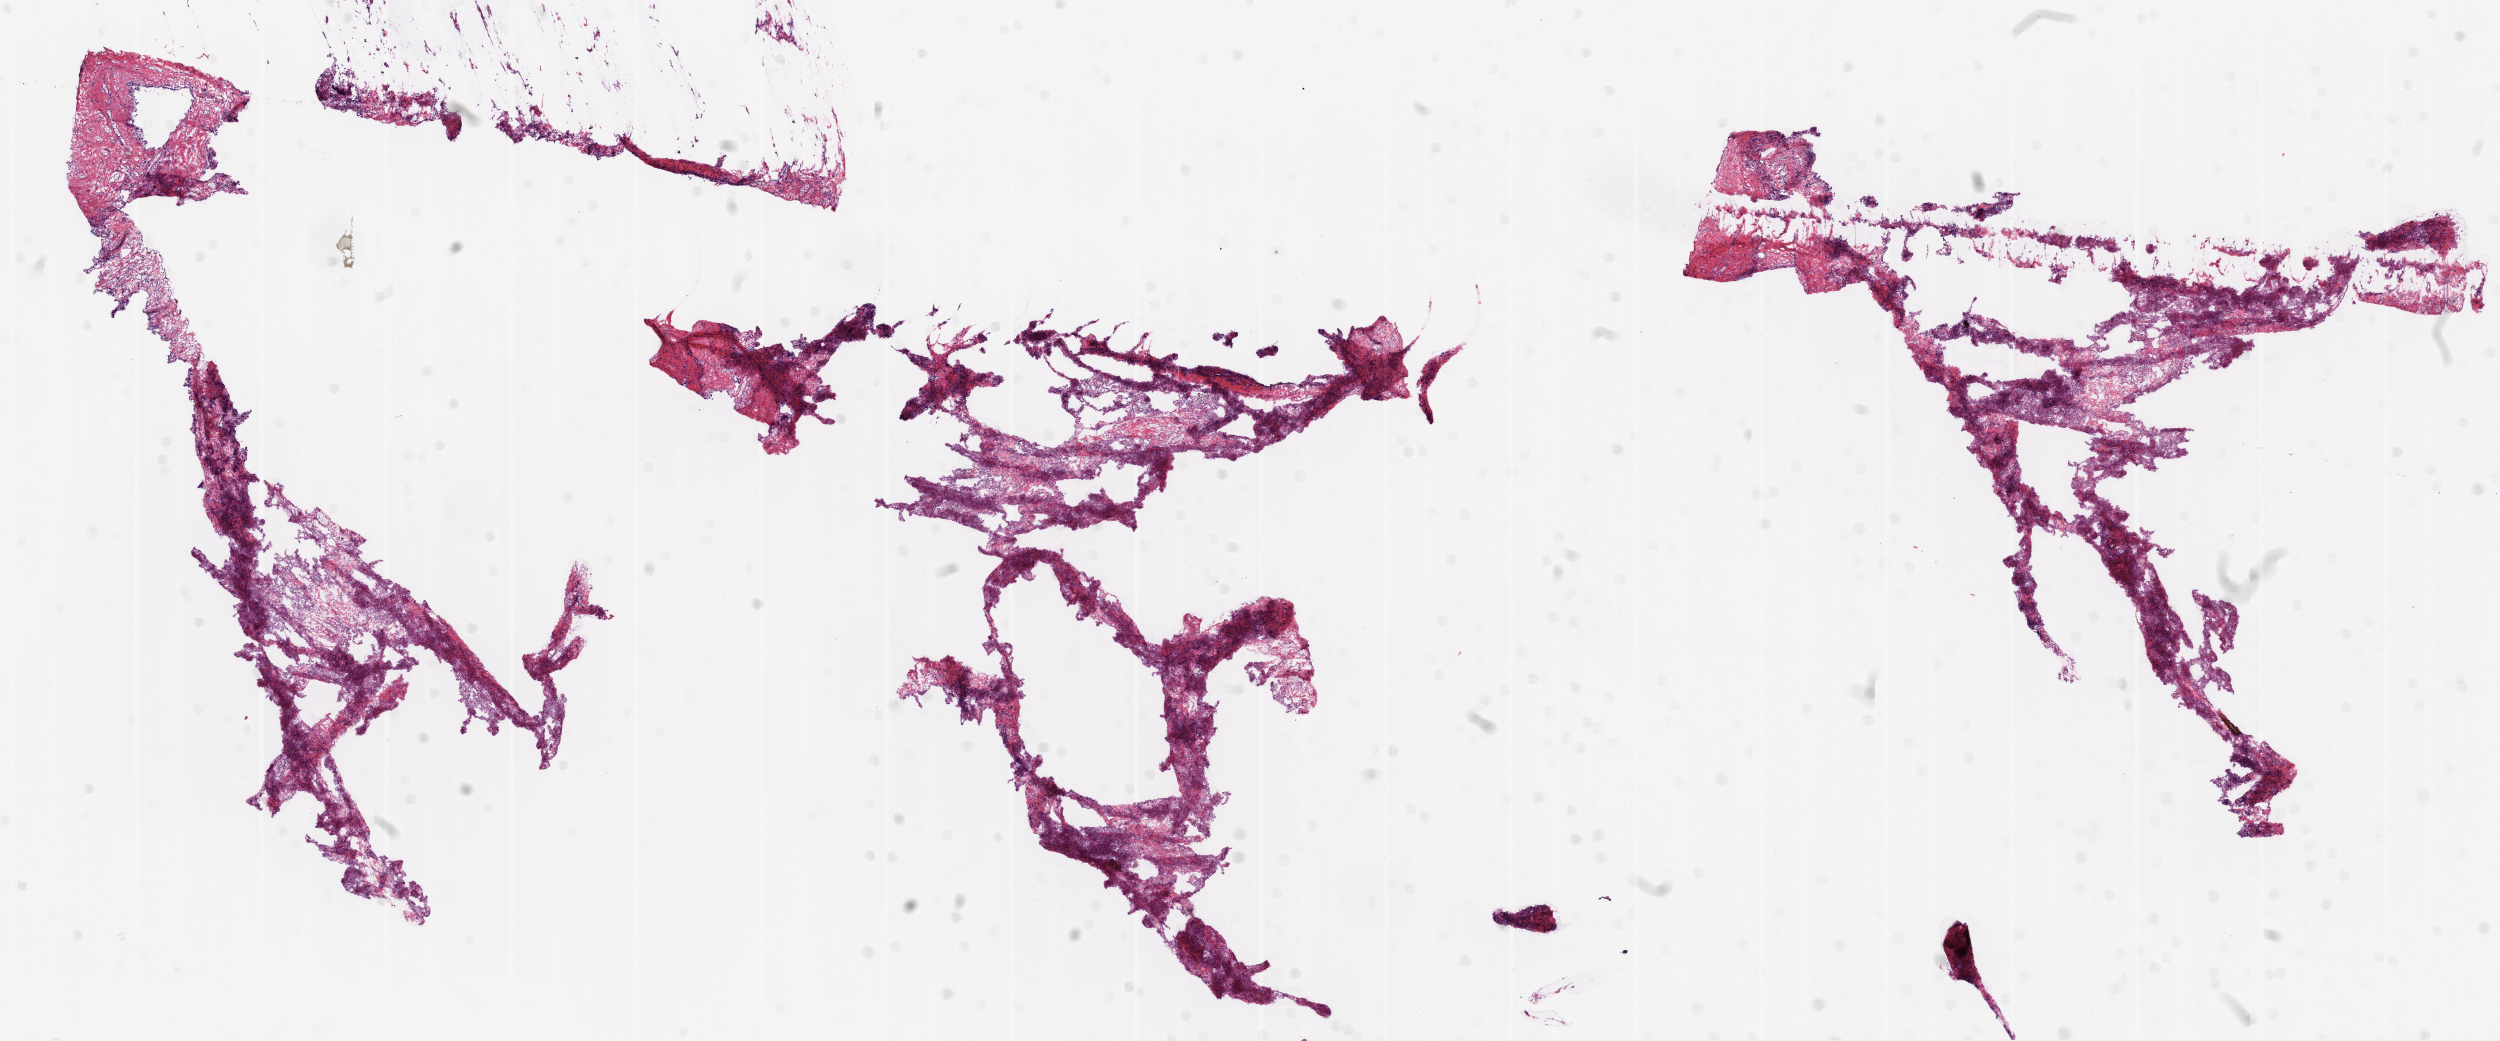
Whole-slide histology image, H&E-stained — whole scanned area (about 20.1 x 8.4 mm, acquisition: 20x scan) shown as a low-resolution overview. Frozen section from the top of the tissue portion. Sample: solid tissue normal (non-tumour tissue), lung. Male, age 62 years at initial diagnosis.
This section: solid tissue normal (non-tumour) sample from the same patient. Patient diagnosis: Squamous cell carcinoma, NOS (lower lobe, lung).